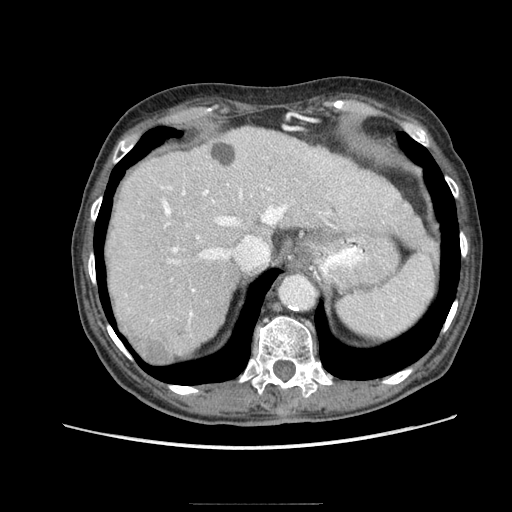
Contrast-enhanced abdominal CT (liver protocol), one axial slice; position 65 of 83 along the scan axis; reconstruction kernel STANDARD; soft-tissue window (W 400 / L 40 HU); 512 × 512 image matrix, field of view 360 × 360 mm. From the clinical record (not read from this slice): diagnosis: hepatocellular carcinoma (patient treated with transarterial chemoembolisation; whether this scan precedes or follows treatment is not stated here); TNM stage (as recorded): Stage-I; Child-Pugh class: A; tumour nodularity: uninodular.
Structures marked on this image (semi-automatically segmented with operator editing):
- abdominal aorta: bounding box (x1, y1, x2, y2) in pixels: (278, 274, 316, 310)
- liver parenchyma outside the tumour (the mass and vessels are separate outlines, so this box may not span the whole liver): (106, 126, 428, 356)
- mass: (143, 337, 171, 366)
- liver vessels: (126, 152, 368, 323)